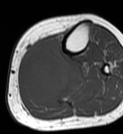
MRI of an extremity soft-tissue mass, one axial slice; MR volume resampled by the dataset authors to the PET/CT grid (not the native acquisition matrix); 3.27 mm slice thickness; 123 × 134 image matrix. Female patient. From the clinical record (not read from this slice): histological type: extraskeletal high grade osteogenic sarcoma; grade: high; site of the primary tumour: left calf.
Annotated regions visible in this slice (expert contour drawn on MRI and transferred to this co-registered scan by the dataset authors):
- gross tumour volume (mass): bounding box <20,39,71,104> (left, top, right, bottom; pixels)